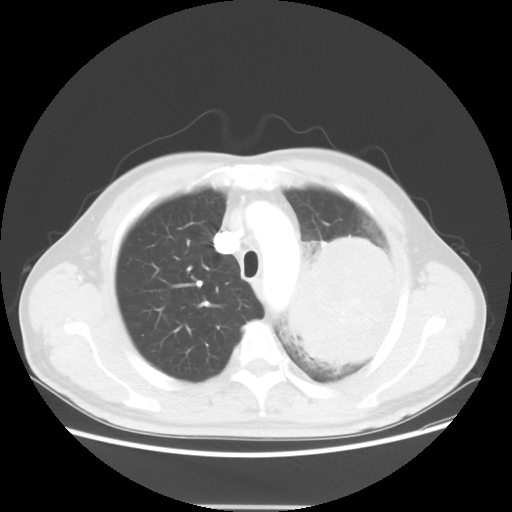
Chest CT, one axial slice. Position 42 of 53 along the scan axis. Lung window (W 1500 / L -600 HU). 5 mm slice thickness. 512 × 512 image matrix. Male patient, age 60 years. From the clinical record (not read from this slice): clinical TNM (as recorded): T4 N1 M1a; histopathological grade: G3.
Structures marked on this image (bounding box drawn by a radiologist):
- lung tumour (recorded histology: large cell carcinoma): bounding box [x1, y1, x2, y2] px = [274, 231, 398, 377]